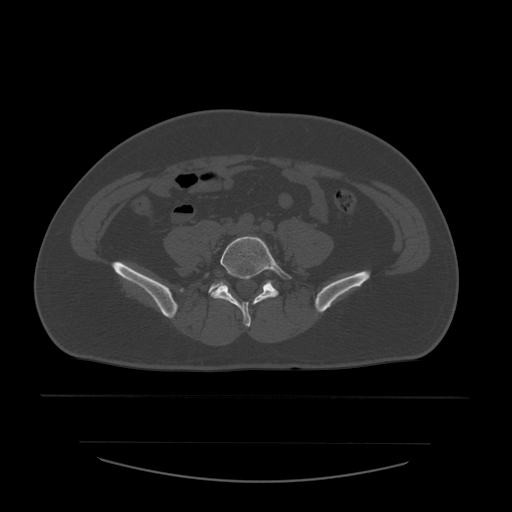
CT including the spine, one axial slice. Position 118 of 532 along the scan axis. Reconstruction kernel STANDARD. 120 kVp. Bone window (W 1800 / L 400 HU). 1.25 mm slice thickness. 512 × 512 image matrix. Patient age 44 years. Case-level facts recorded for this patient, not image findings: primary cancer: soft tissue sarcoma.
Outlined on this slice (semi-automatic segmentation, software-assisted and operator-edited):
- L5 vertebra: bounding box [x1, y1, x2, y2] px = [206, 237, 292, 327]